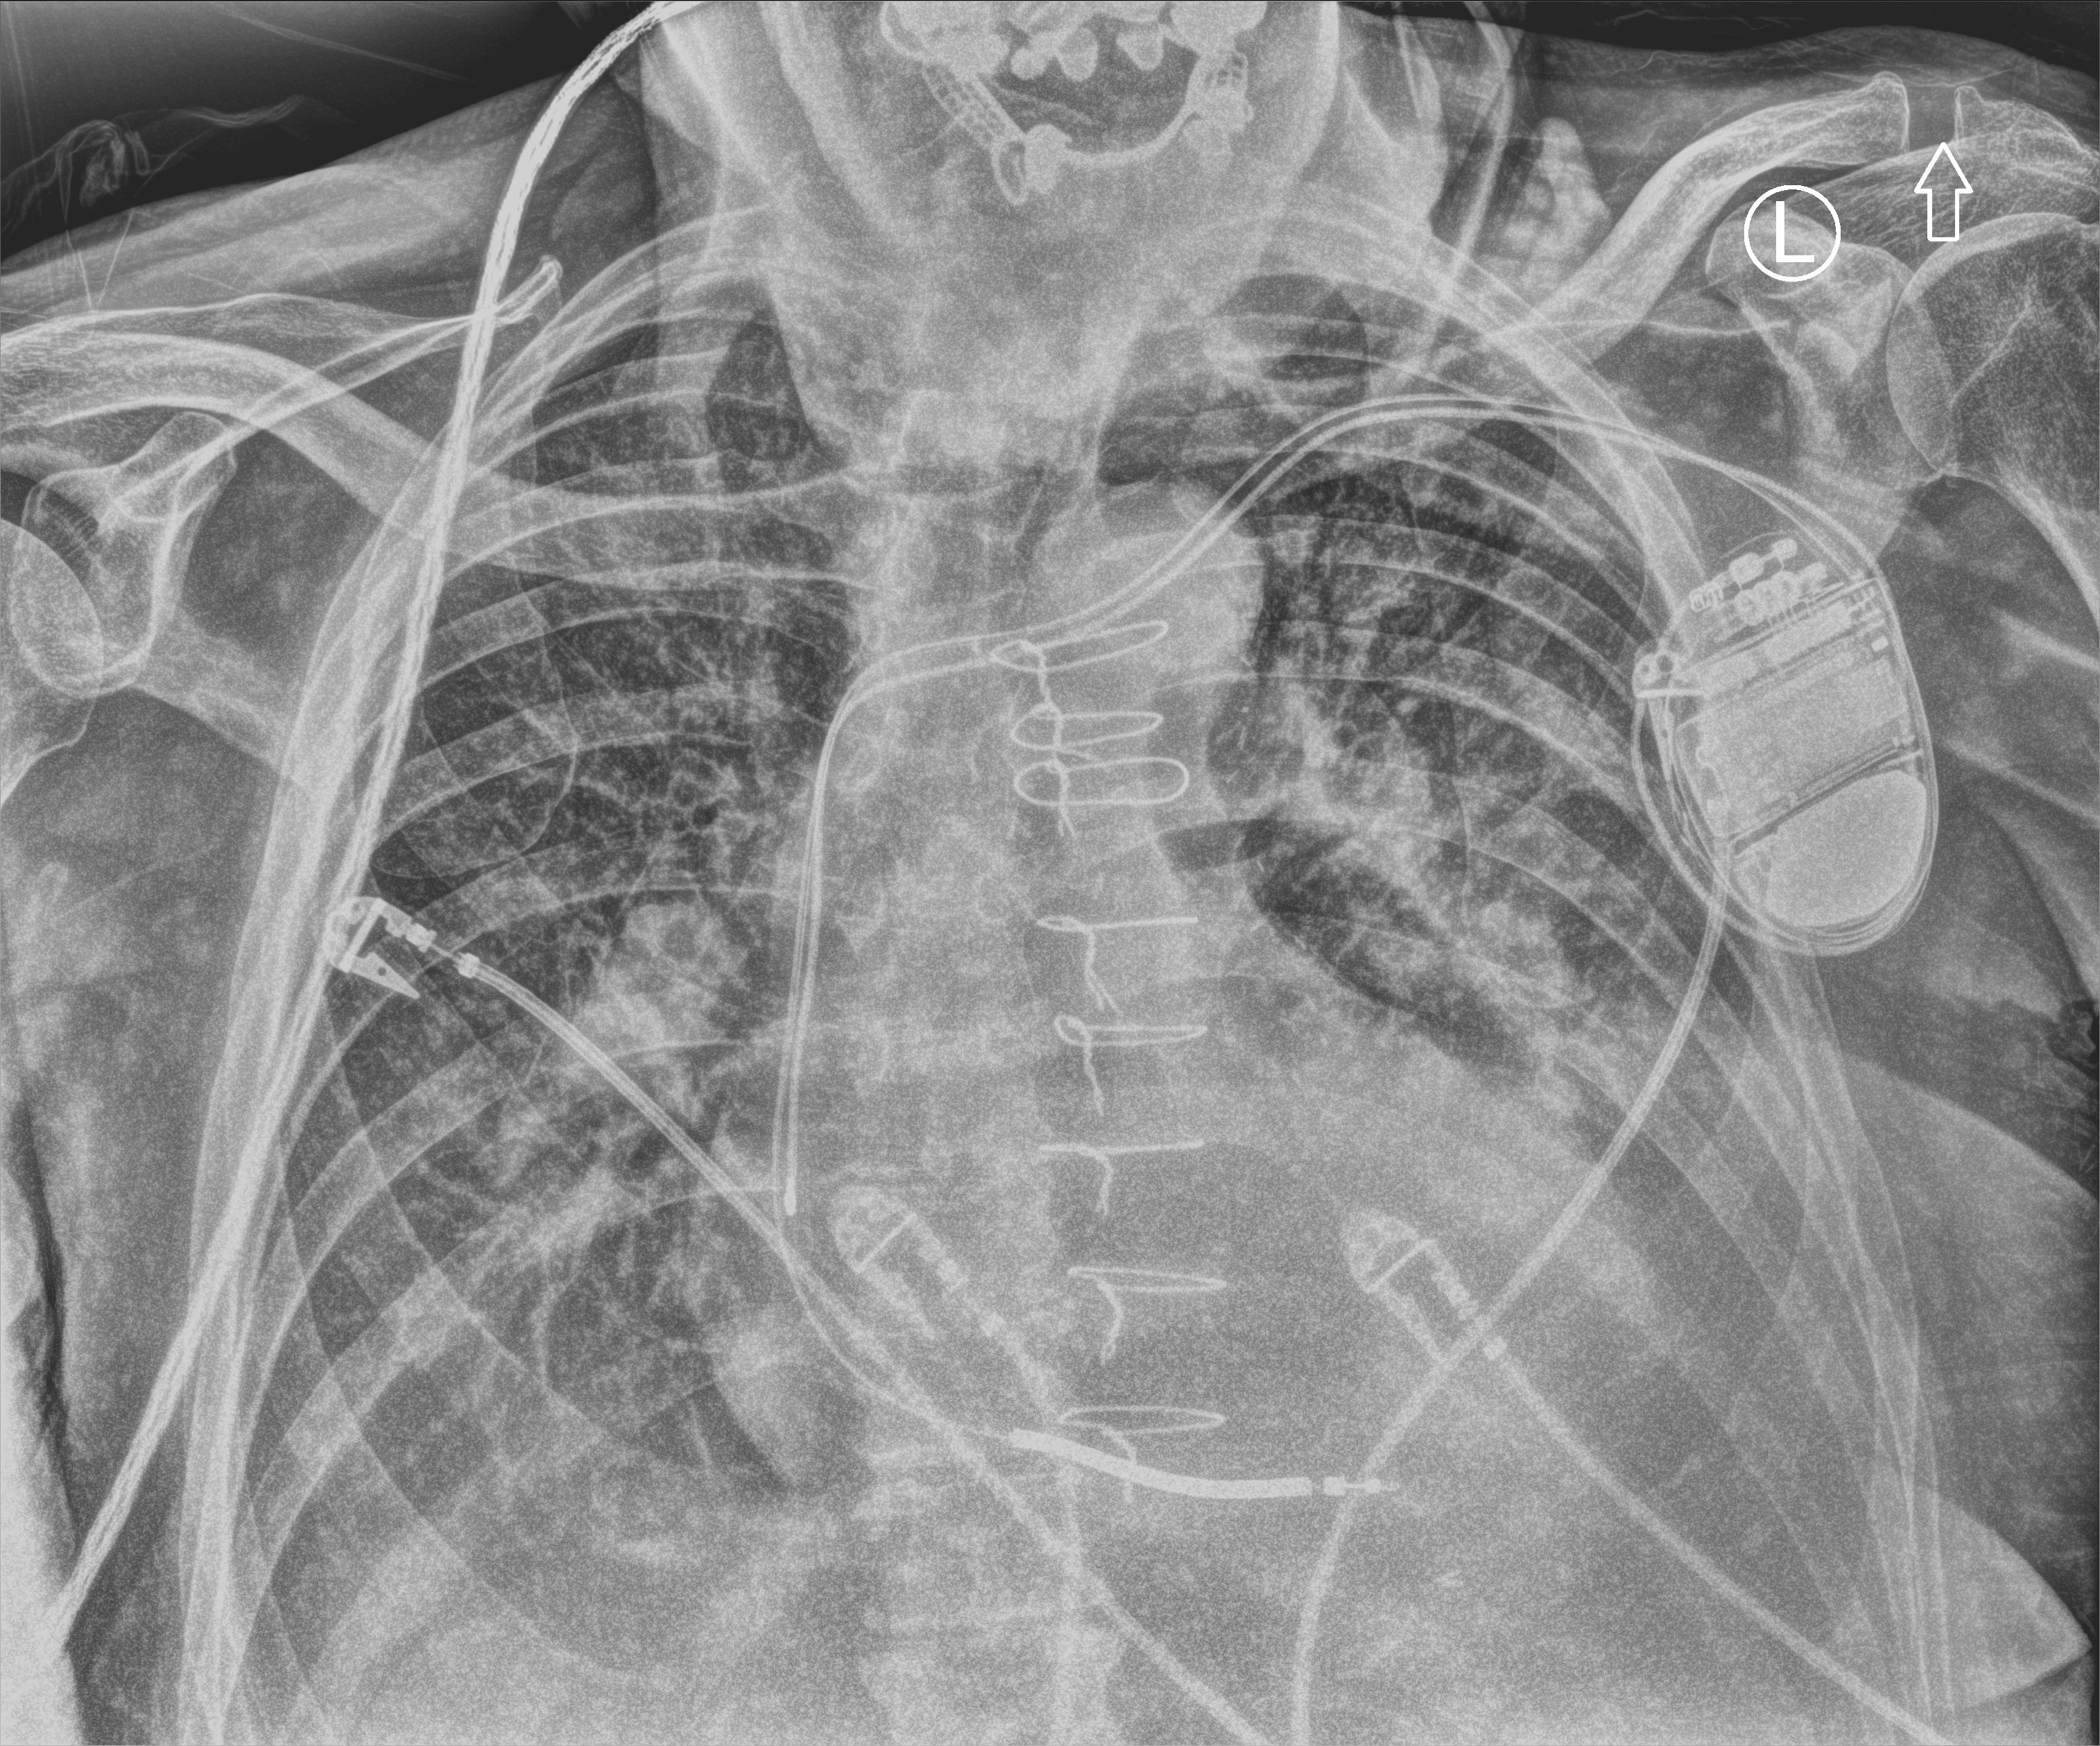
Portable chest radiograph, anteroposterior (AP) projection. Patient hospitalised with COVID-19; male, aged 75–90 years.
From the hospital-stay record, not from the radiograph (when in the stay this image was taken is not recorded): mechanically ventilated during this hospital stay: yes.